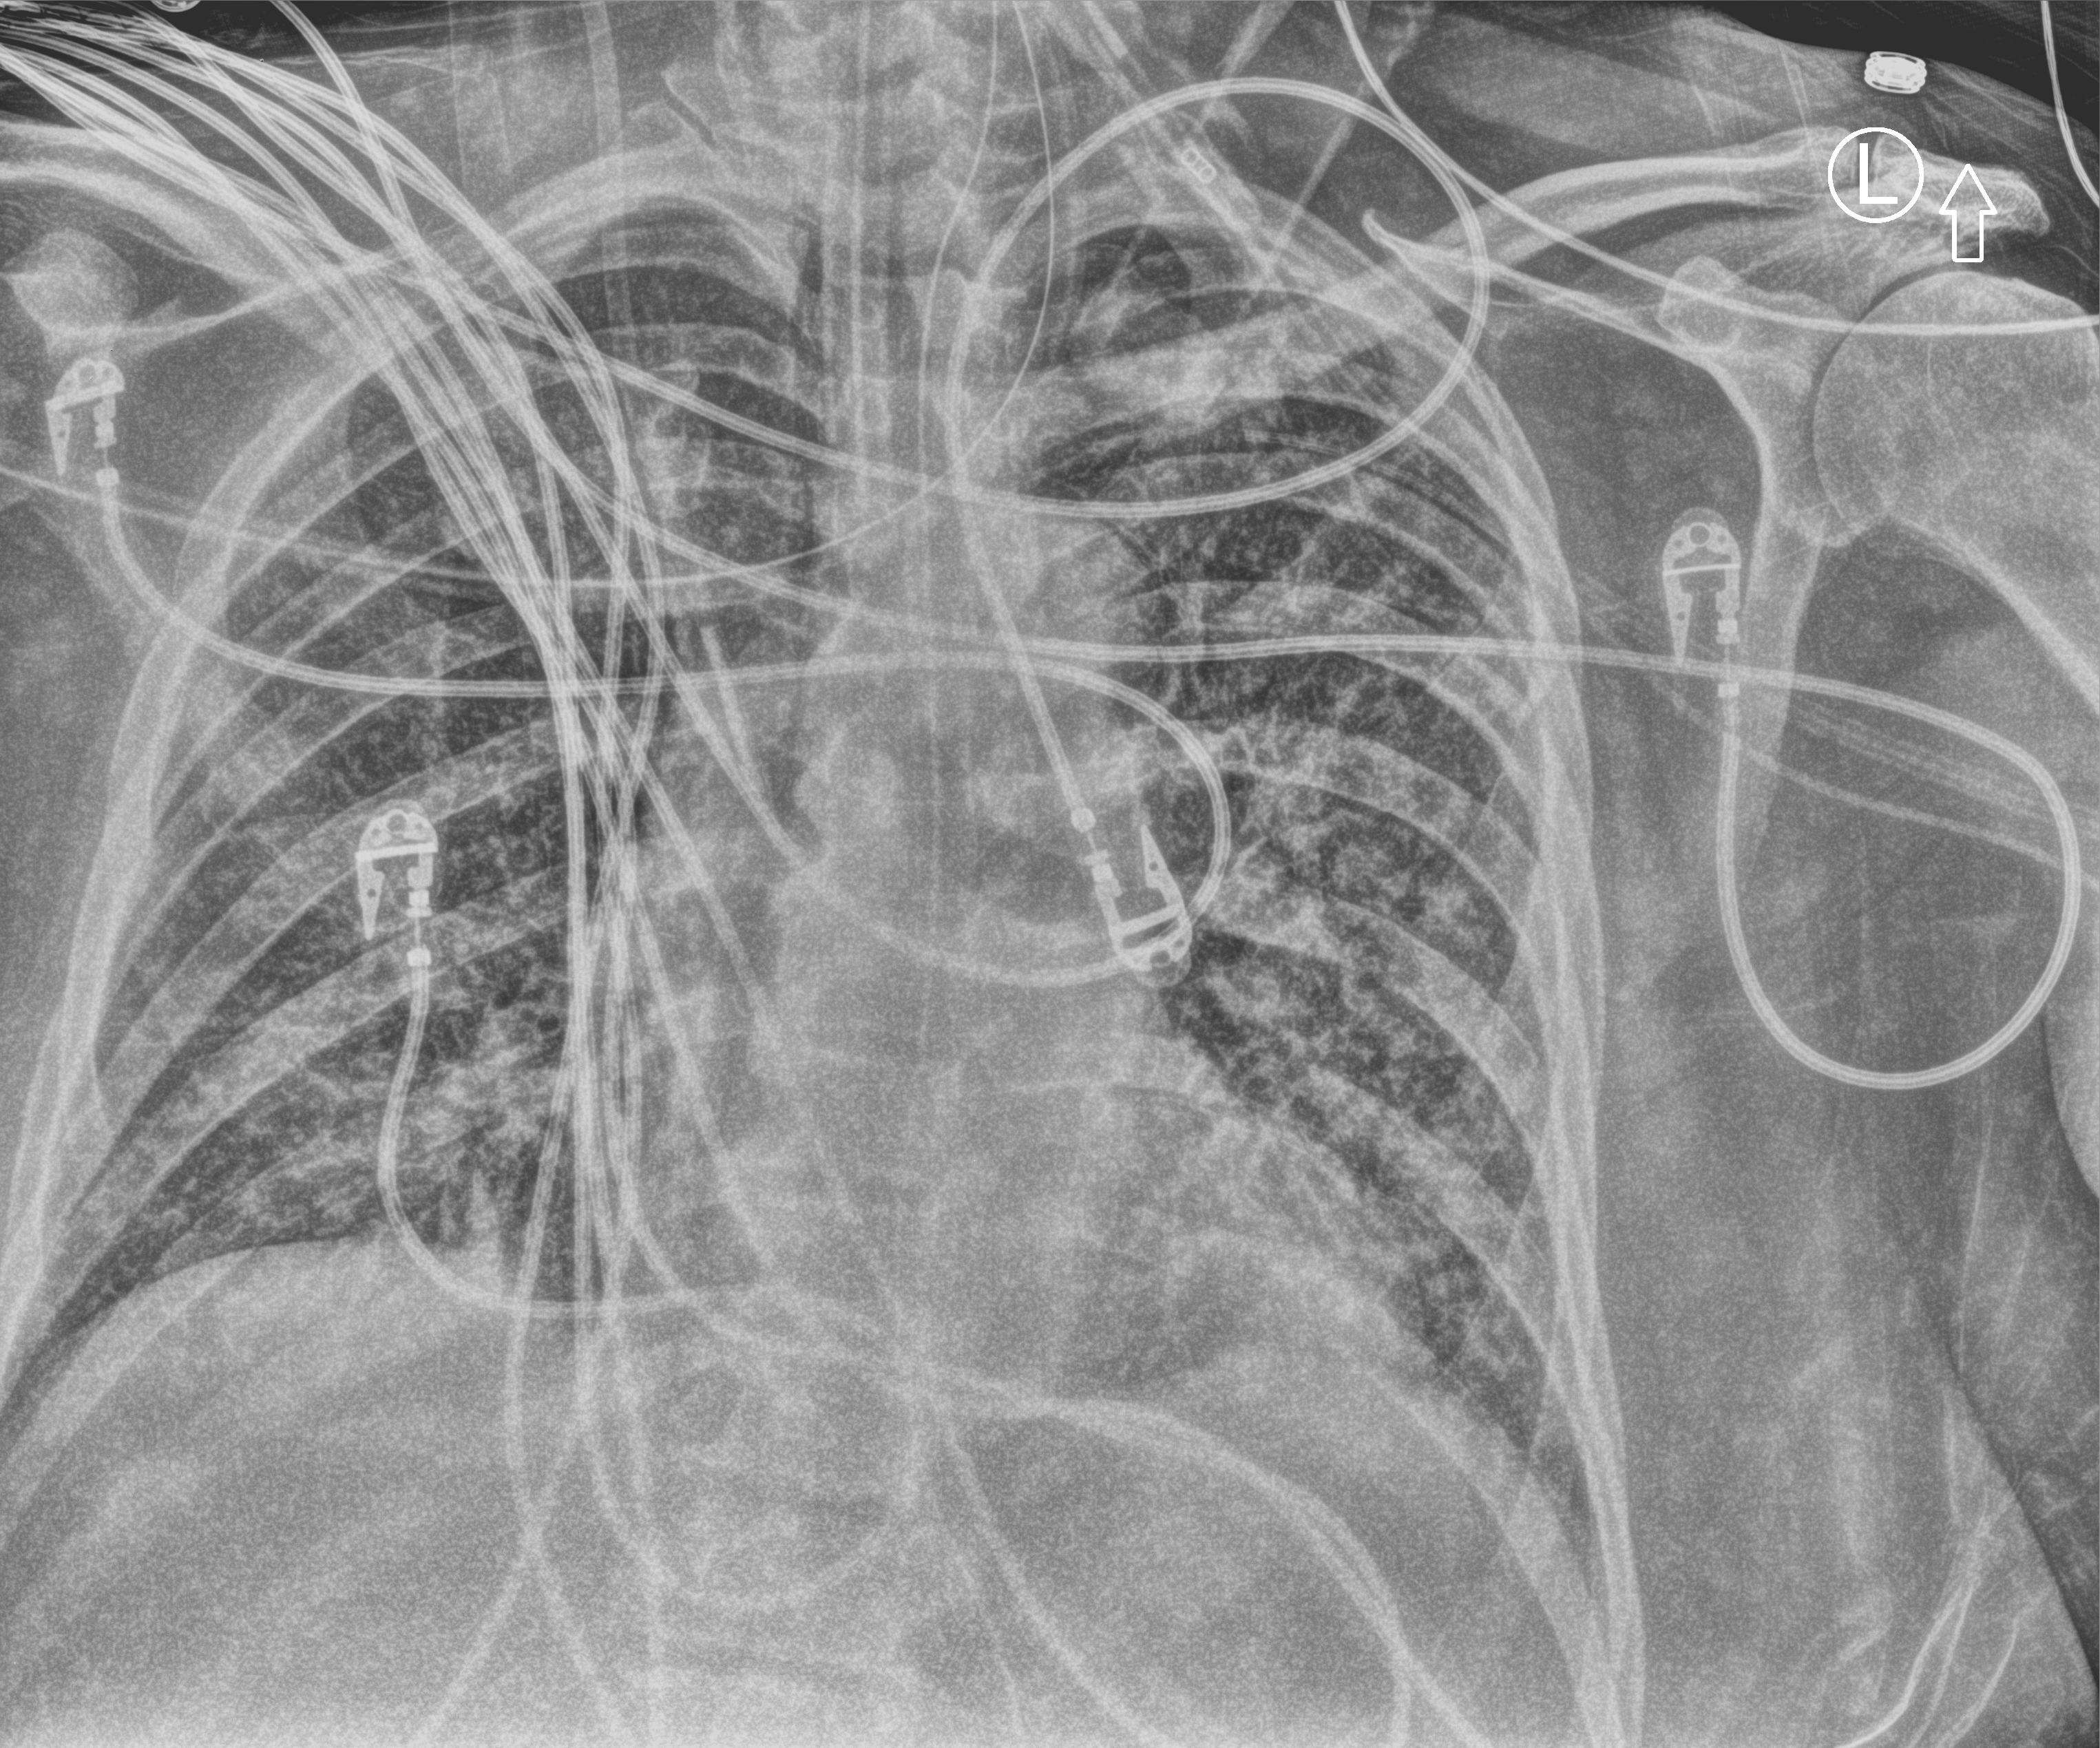
Bedside chest radiograph (computed radiography); anteroposterior (AP) projection. Male patient hospitalised with COVID-19, age 60–74 years.
Admission-level facts for this patient (not findings on this image; timing relative to this image not recorded):
- mechanically ventilated during this hospital stay: yes